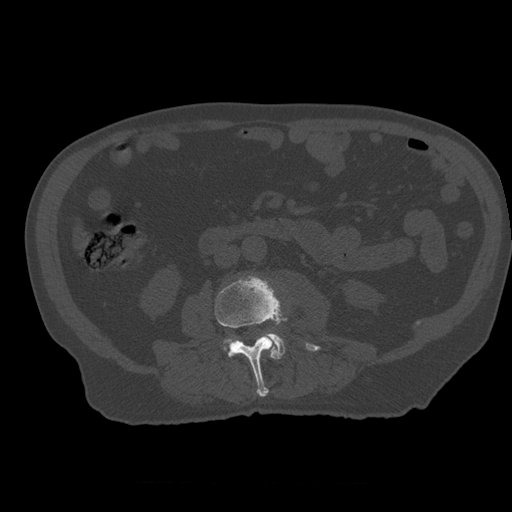
CT including the spine, one axial slice; slice 185 of 399 in the series (ordered by position); reconstruction kernel STANDARD; bone window (W 1800 / L 400 HU); 512 × 512 image matrix, field of view 407 × 407 mm. Patient age 73 years. Case-level facts recorded for this patient, not image findings: primary cancer: prostate.
Outlined on this slice (semi-automatic segmentation, software-assisted and operator-edited):
- L2 vertebra: bounding box <260,350,264,356> (left, top, right, bottom; pixels)
- L3 vertebra: <215,276,321,397>
- L4 vertebra: <223,334,285,356>